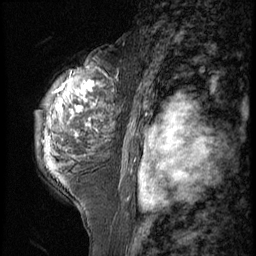
Breast MRI (dynamic contrast-enhanced), one sagittal slice. 3 images stored at this slice position (order not interpretable as contrast timing). 1.5 T. TE 4.2 ms, TR 9 ms. 2.5 mm slice thickness. 256 × 256 image matrix, field of view 180 × 180 mm. Patient: female, 50 years. From the clinical record (not read from this slice): setting: breast cancer imaged before/during neoadjuvant chemotherapy; receptor status: triple-negative.
Structures marked on this image (semi-automatically segmented with operator editing):
- analysis volume of interest (the breast-tissue region the enhancement analysis was run in; not a lesion): bounding box [x1, y1, x2, y2] px = [34, 50, 124, 191]
- tumour enhancement mask (voxels above the 140 % enhancement threshold inside the analysis volume of interest): [69, 81, 96, 126]